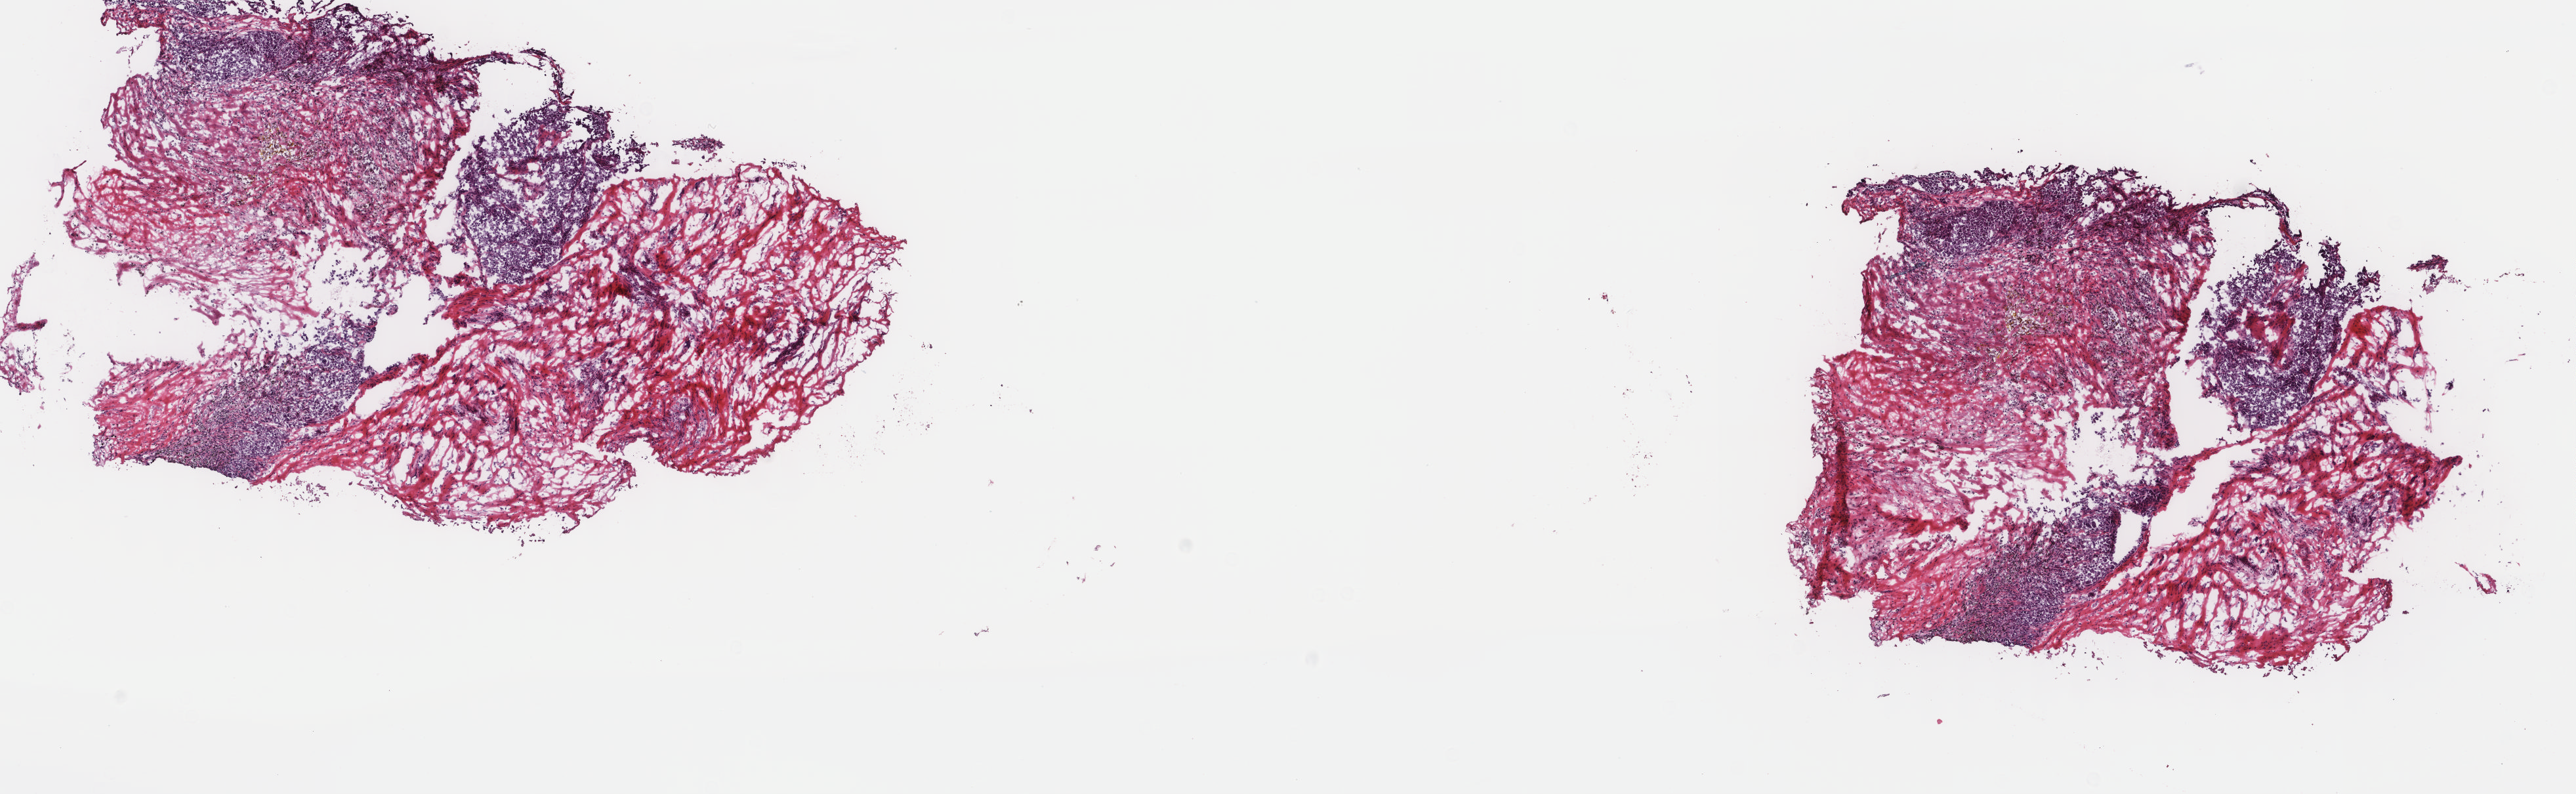
H&E whole-slide image — low-resolution overview of the scanned area, about 15.6 x 4.8 mm (from a 40x scan). Frozen section from the top of the tissue portion. Metastatic tumour sample. Male patient; age at initial diagnosis 51 years. Composition of this section per pathologist review: tumour cells 70%, tumour nuclei 70%, normal cells 0%, stromal cells 30%, necrosis 0%. Infiltration values recorded for this section: lymphocyte infiltration 7%, monocyte infiltration 0%, neutrophil infiltration 0%.
This section: metastatic tumour tissue. Patient diagnosis: Malignant melanoma, NOS.